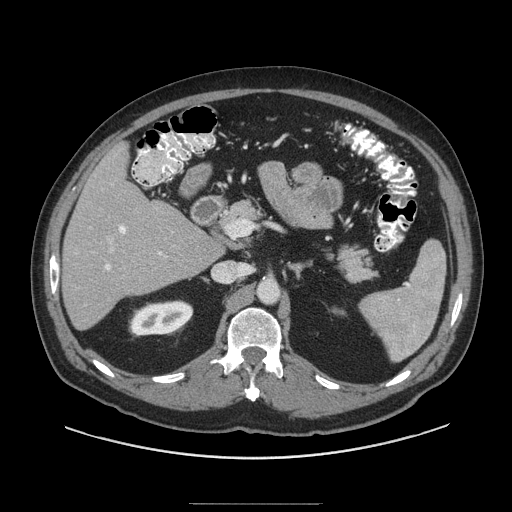
Contrast-enhanced abdominal CT (liver protocol), one axial slice; position 50 of 91 along the scan axis; reconstruction kernel STANDARD; 140 kVp; soft-tissue window (W 400 / L 40 HU); 512 × 512 image matrix, field of view 440 × 440 mm. From the clinical record (not read from this slice): diagnosis: hepatocellular carcinoma (patient treated with transarterial chemoembolisation; whether this scan precedes or follows treatment is not stated here); TNM stage (as recorded): Stage-I; Child-Pugh class: A; tumour differentiation: well differentiated; tumour size: 4 cm.
Outlined on this slice (semi-automatically segmented with operator editing):
- liver parenchyma outside the tumour (the mass and vessels are separate outlines, so this box may not span the whole liver): bounding box (x1, y1, x2, y2) in pixels: (62, 142, 222, 330)
- liver vessels: (105, 225, 162, 270)